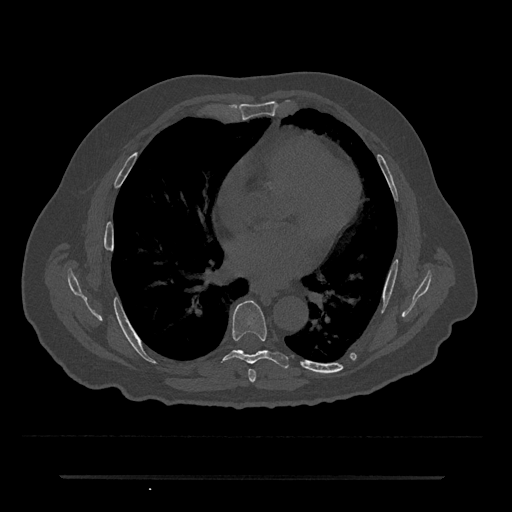
CT including the spine, one axial slice. Slice 387 of 797 in the series (ordered by position). Bone window (W 1800 / L 400 HU). 512 × 512 image matrix, field of view 437 × 437 mm. Male patient, age 69 years. From the clinical record (not read from this slice): primary cancer: prostate.
Outlined on this slice (semi-automatic segmentation, software-assisted and operator-edited):
- T6 vertebra: bounding box (x1, y1, x2, y2) in pixels: (248, 369, 256, 383)
- T7 vertebra: (224, 300, 289, 368)